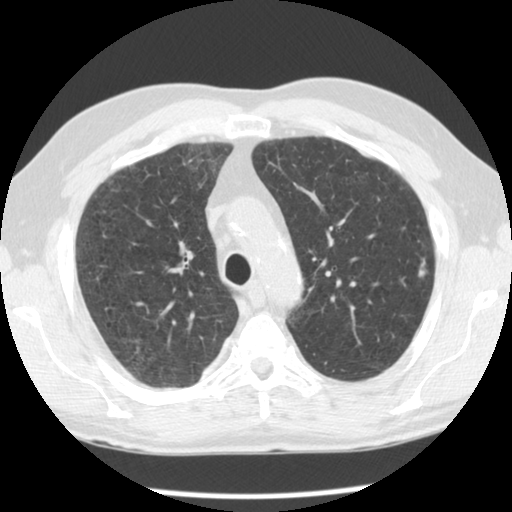
Low-dose screening chest CT, one axial slice. Slice 85 of 113 in the series (ordered by position). Lung window (W 1500 / L -600 HU). 2.5 mm slice thickness. 512 × 512 image matrix, field of view 330 × 330 mm.
Outlined on this slice (expert manual segmentation):
- lesion 3 (tumor, upper lobe of left lung): bounding box [x1, y1, x2, y2] px = [418, 258, 426, 277]